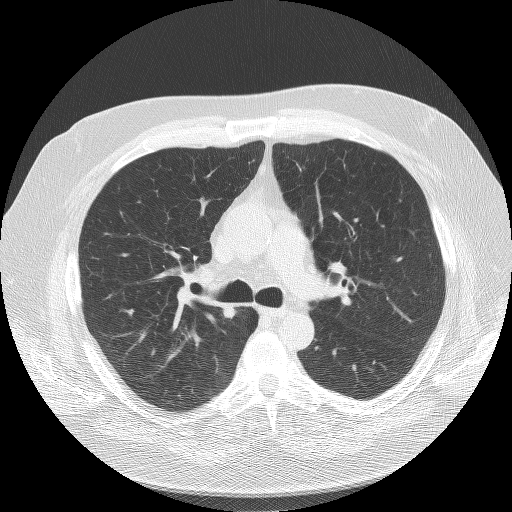
Chest CT (low-dose screening protocol), one axial image. Third annual screen. Lung window (W 1500 / L -600 HU). 2.5 mm slice thickness. Lung (sharp) reconstruction kernel (BONE). 512 × 512 image matrix. Male, age 58 years at enrolment. Former smoker at enrolment.
Expert reader's lesion annotation, bounding box [x1, y1, x2, y2] px = [202, 288, 254, 338]. Reader record for this screening exam (exam-level; its link to the box is not recorded): non-calcified nodule or mass ≥4 mm, right upper lobe, 9 × 8 mm, spiculated (stellate) margins, soft tissue attenuation, pre-existing on the prior screen: yes; interval growth: yes. Later outcome: lung cancer diagnosed 157 days after this screen — squamous cell carcinoma, NOS, right upper lobe, moderately differentiated (G2), stage IA (AJCC 6th edition), 18 mm at pathology.